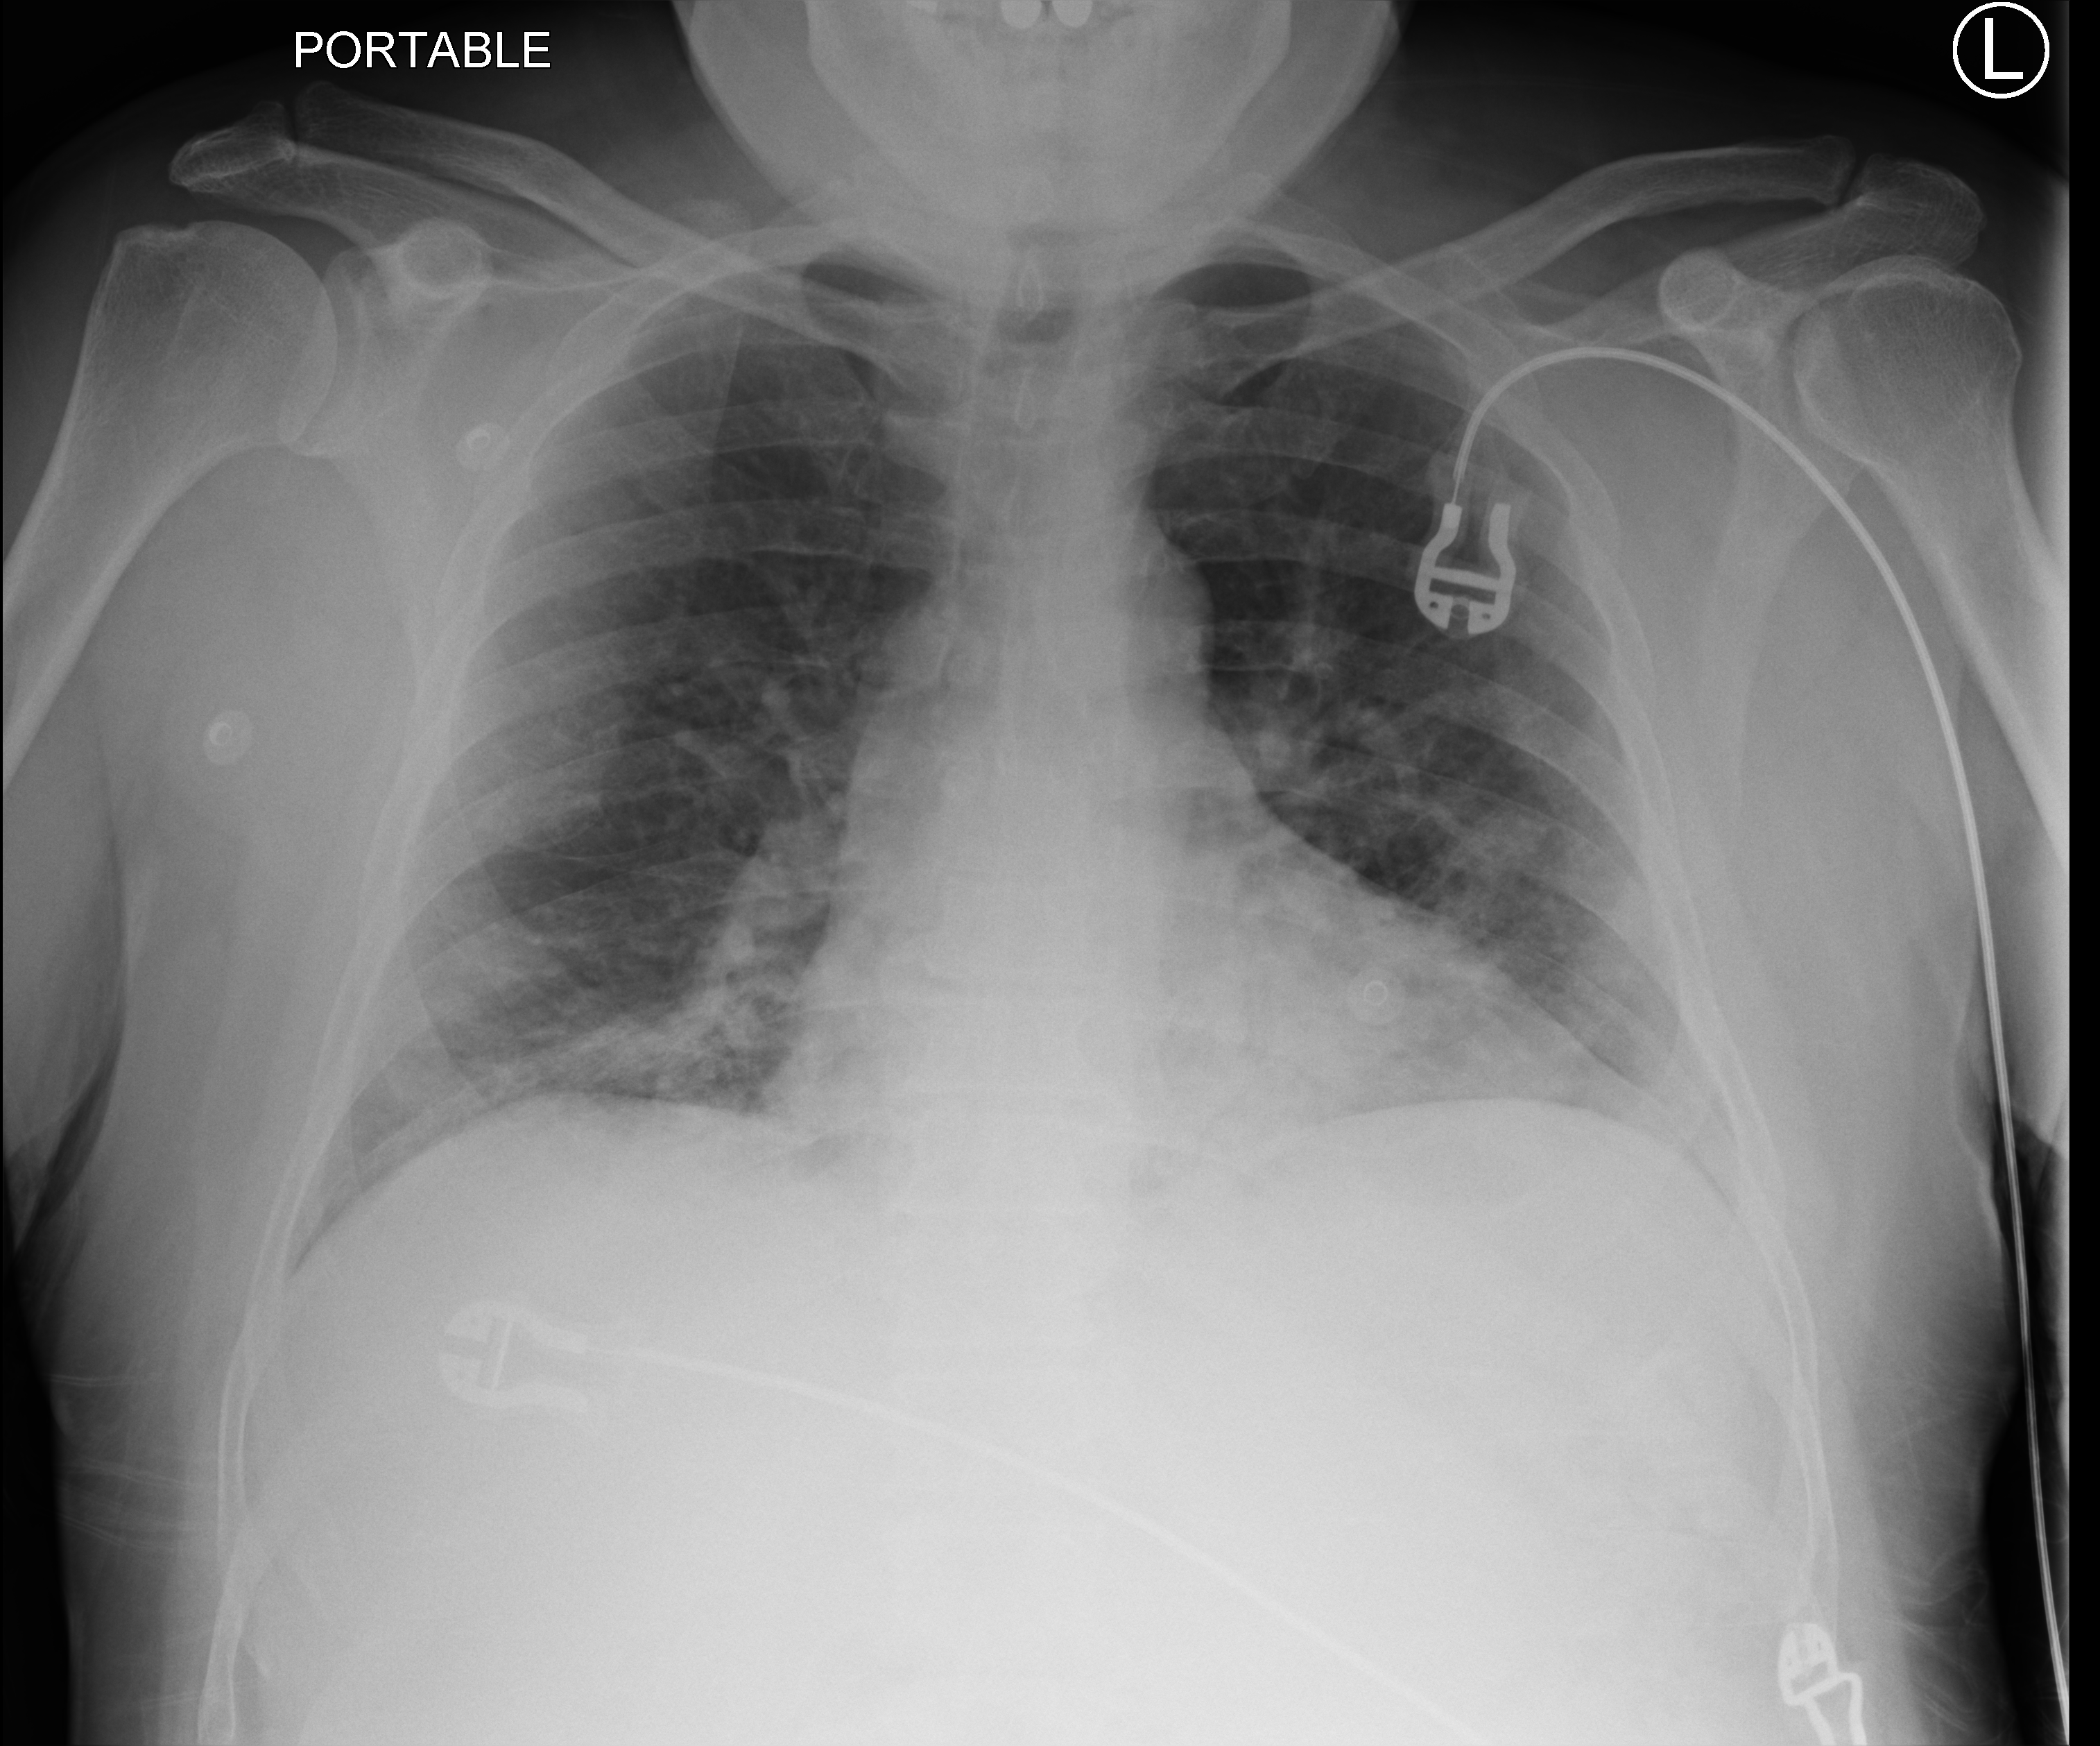
Portable chest radiograph. Patient hospitalised with COVID-19; male, aged 18–59 years.
Hospital-stay facts (about this admission, not read from this image; timing relative to this image not recorded): mechanically ventilated during this hospital stay: yes; admitted to intensive care during this hospital stay: yes.